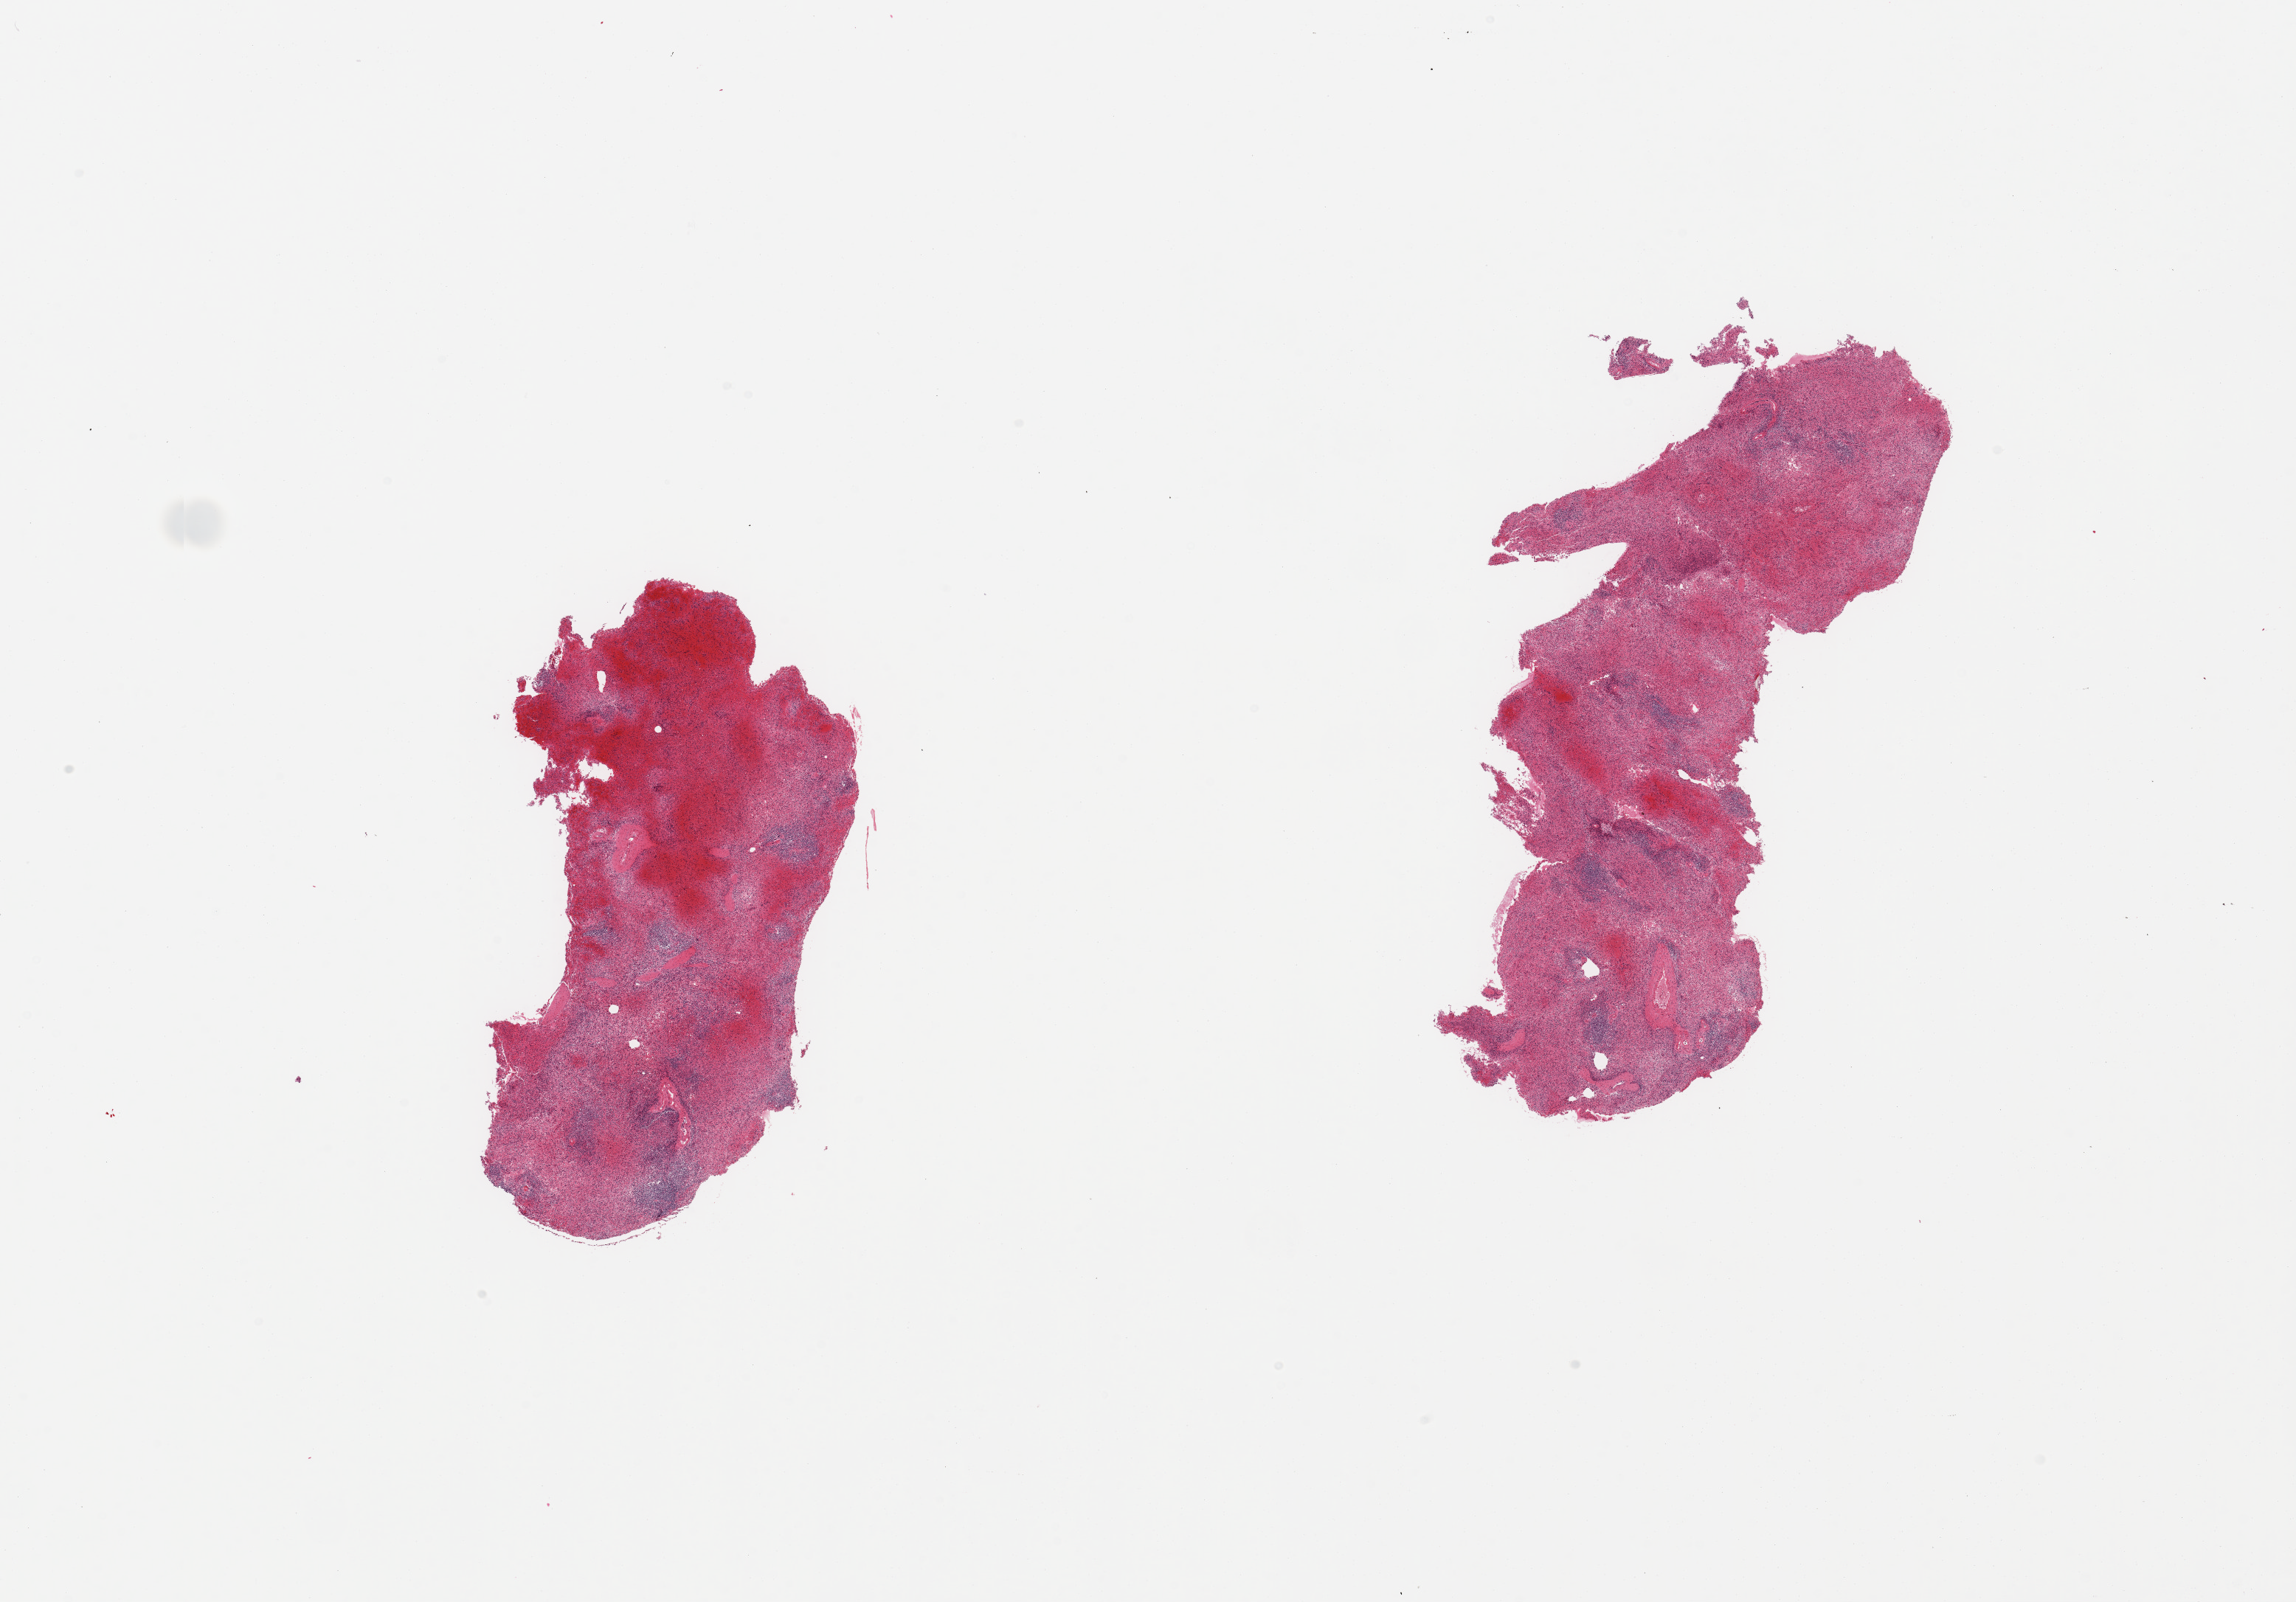
Digitized H&E-stained section, brightfield — shown as a low-resolution overview of the whole scanned area (about 24.6 x 17.2 mm). PAXgene-fixed paraffin-embedded (PFPE) section. Sampled site (target tissue): spleen. Tissue donor sample. Male donor.
Review note (as recorded): 2 pieces, marked congestion.